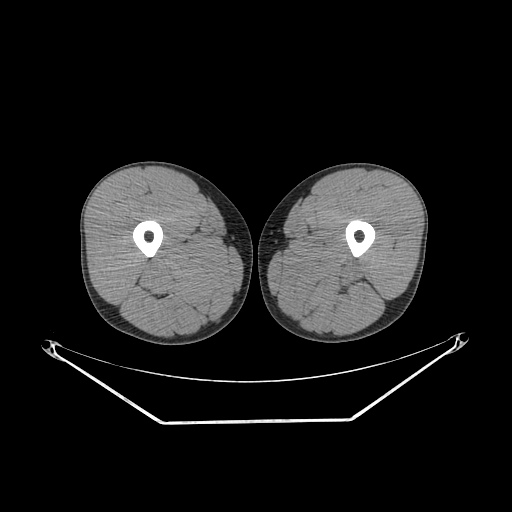
CT of an extremity soft-tissue mass (from a PET/CT study), one axial slice; slice 230 of 267 in the series (ordered by position); 140 kVp; soft-tissue window (W 400 / L 40 HU); 3.75 mm slice thickness; 512 × 512 image matrix, field of view 500 × 500 mm. Male patient. From the clinical record (not read from this slice): histological type: extraskeletal osteosarcoma; grade: high; site of the primary tumour: left adductur.
Structures marked on this image (expert contour drawn on MRI and transferred to this co-registered scan by the dataset authors):
- gross tumour volume (mass): bounding box <269,244,369,312> (left, top, right, bottom; pixels)